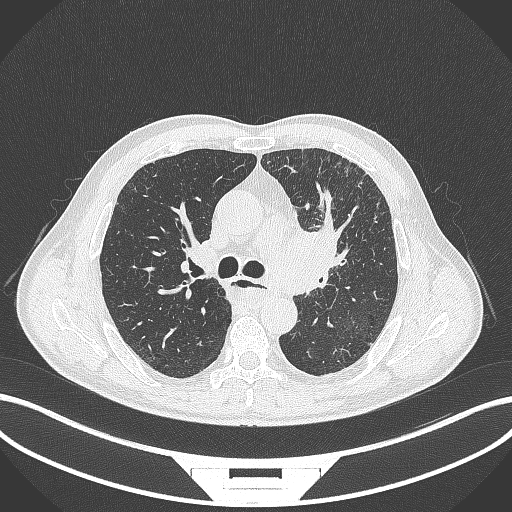
Chest CT, one axial slice; position 245 of 411 along the scan axis; reconstruction kernel B70f; 120 kVp; lung window (W 1500 / L -600 HU); 1 mm slice thickness; 512 × 512 image matrix. Male patient, age 57 years. Case-level facts recorded for this patient, not image findings: clinical TNM (as recorded): T2a N1 M0.
Outlined on this slice (rectangle marked by the reading radiologist):
- lung tumour (recorded histology: squamous cell carcinoma): bounding box [x1, y1, x2, y2] px = [272, 215, 355, 295]